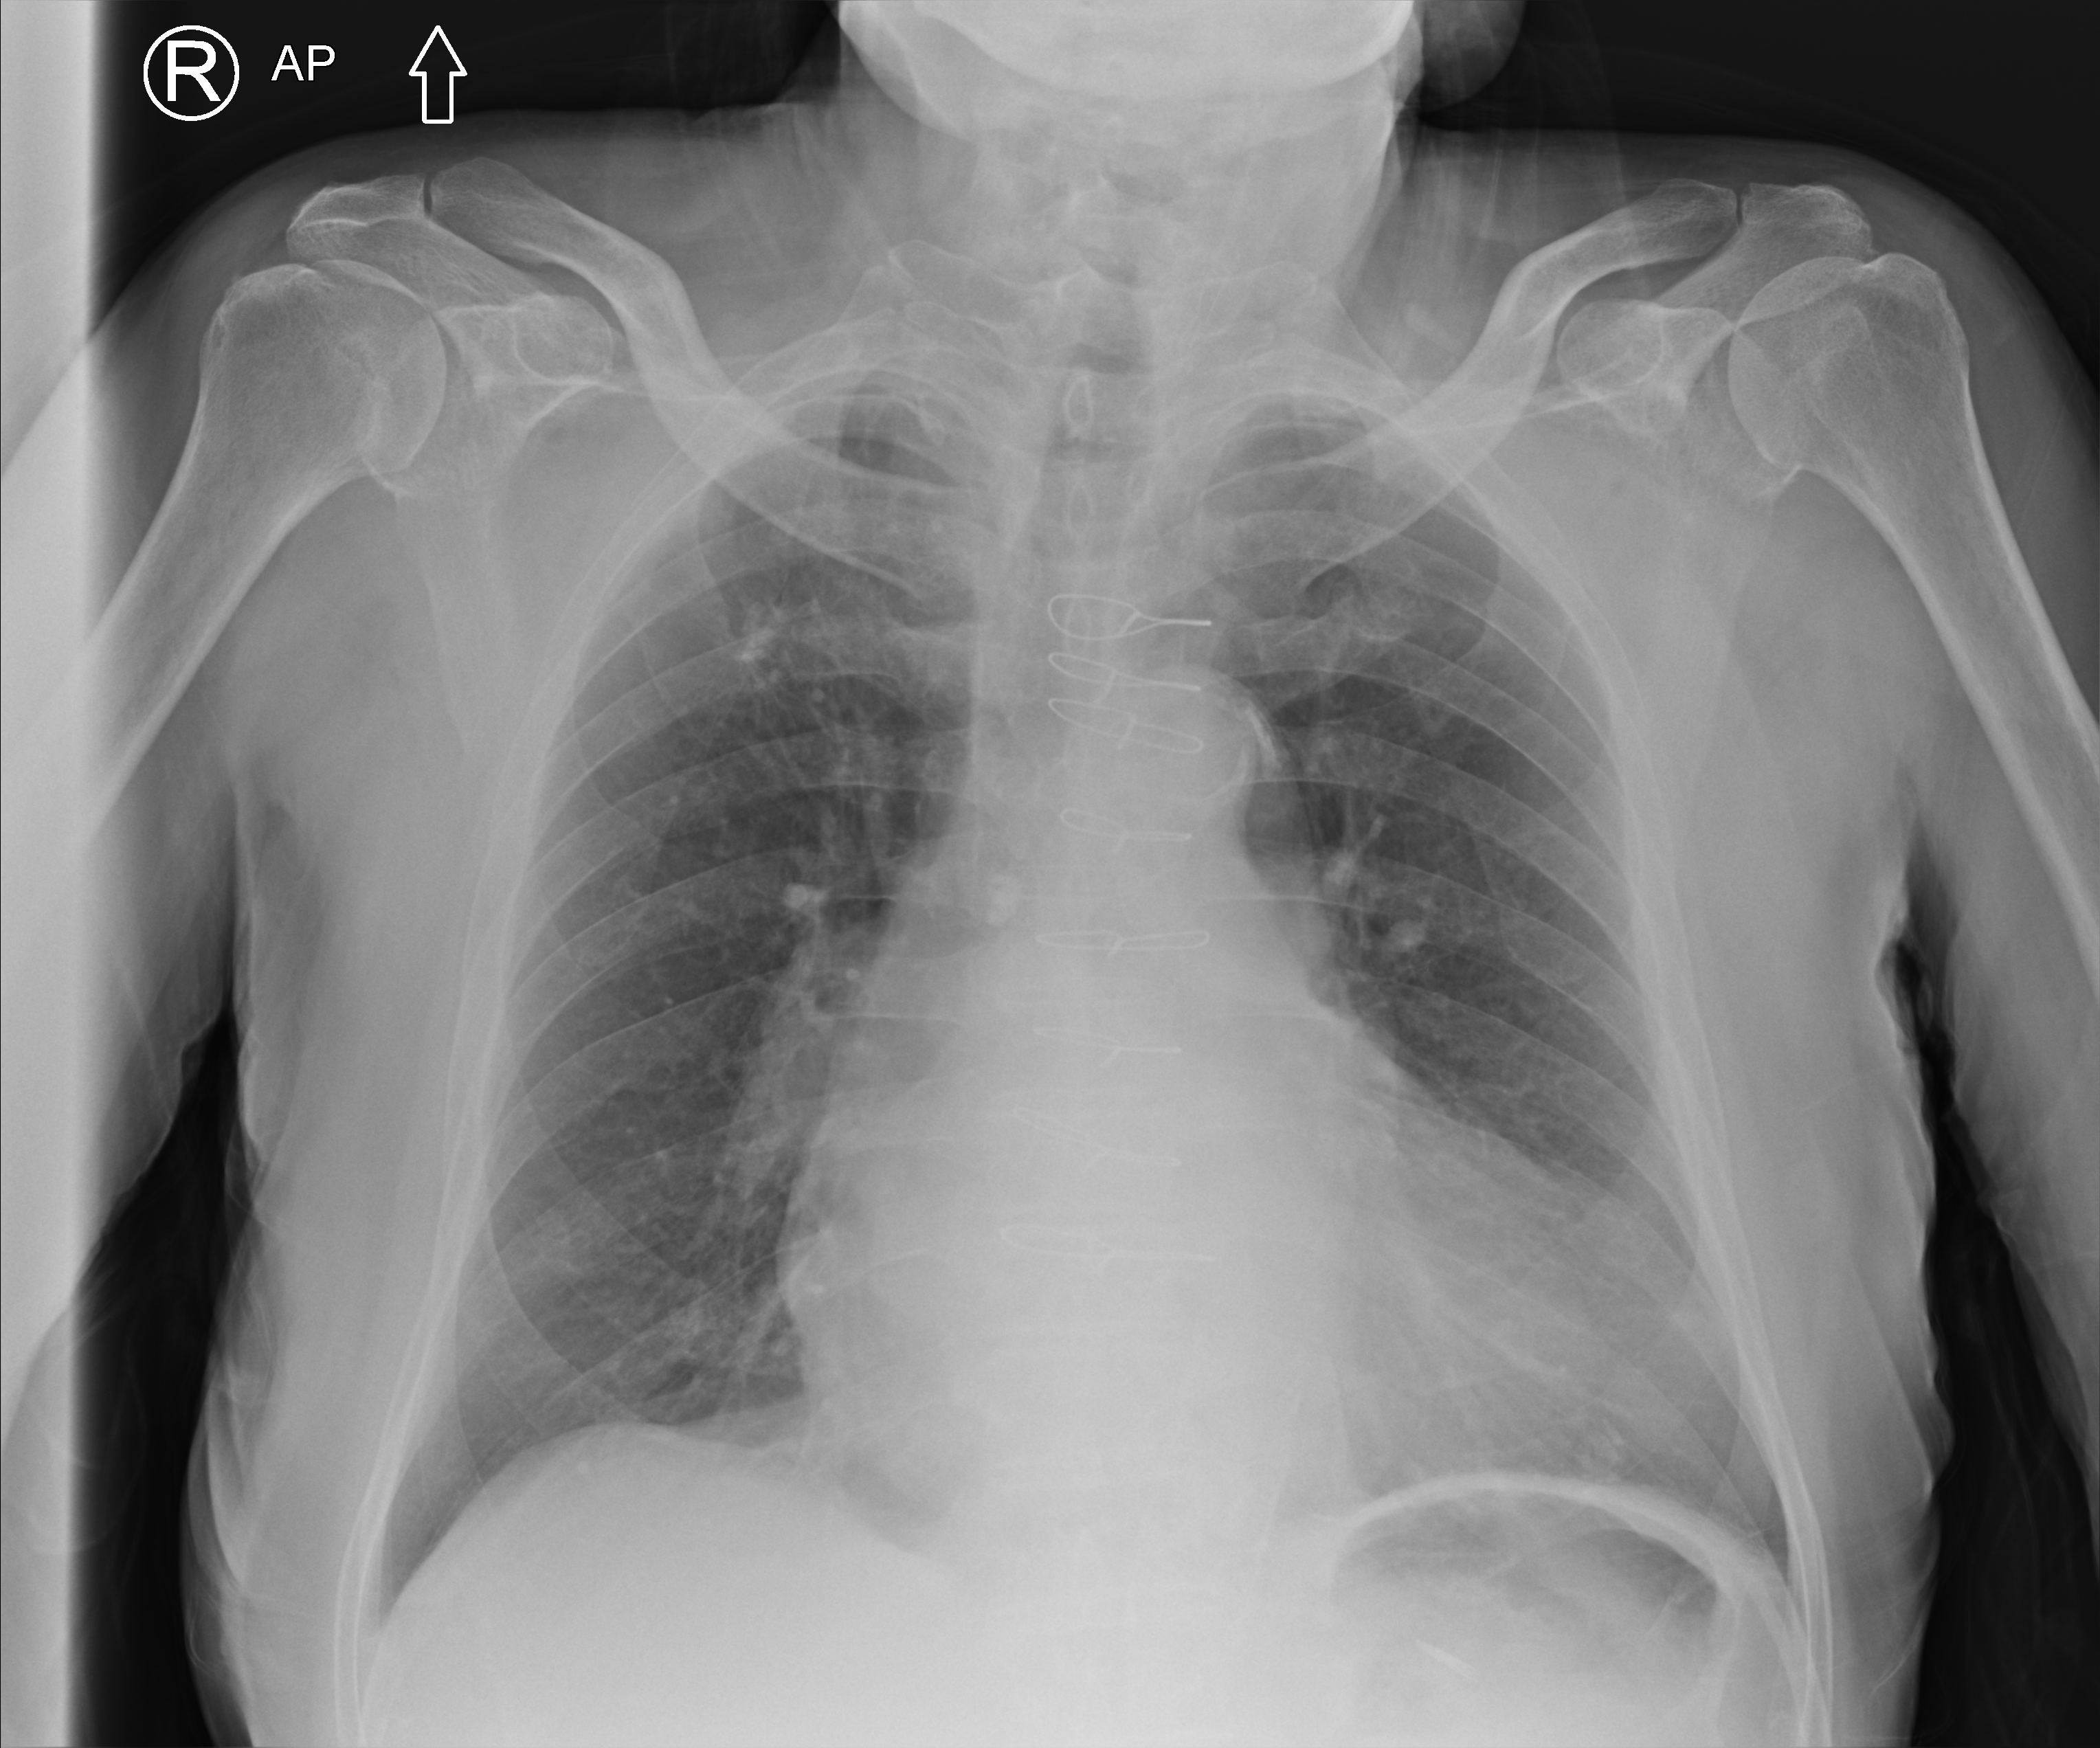
Bedside chest radiograph (computed radiography). Patient hospitalised with COVID-19; male, aged 75–90 years.
From the hospital-stay record, not from the radiograph (when in the stay this image was taken is not recorded):
- diabetes (admission record): yes
- admitted to intensive care during this hospital stay: no
- mechanically ventilated during this hospital stay: no